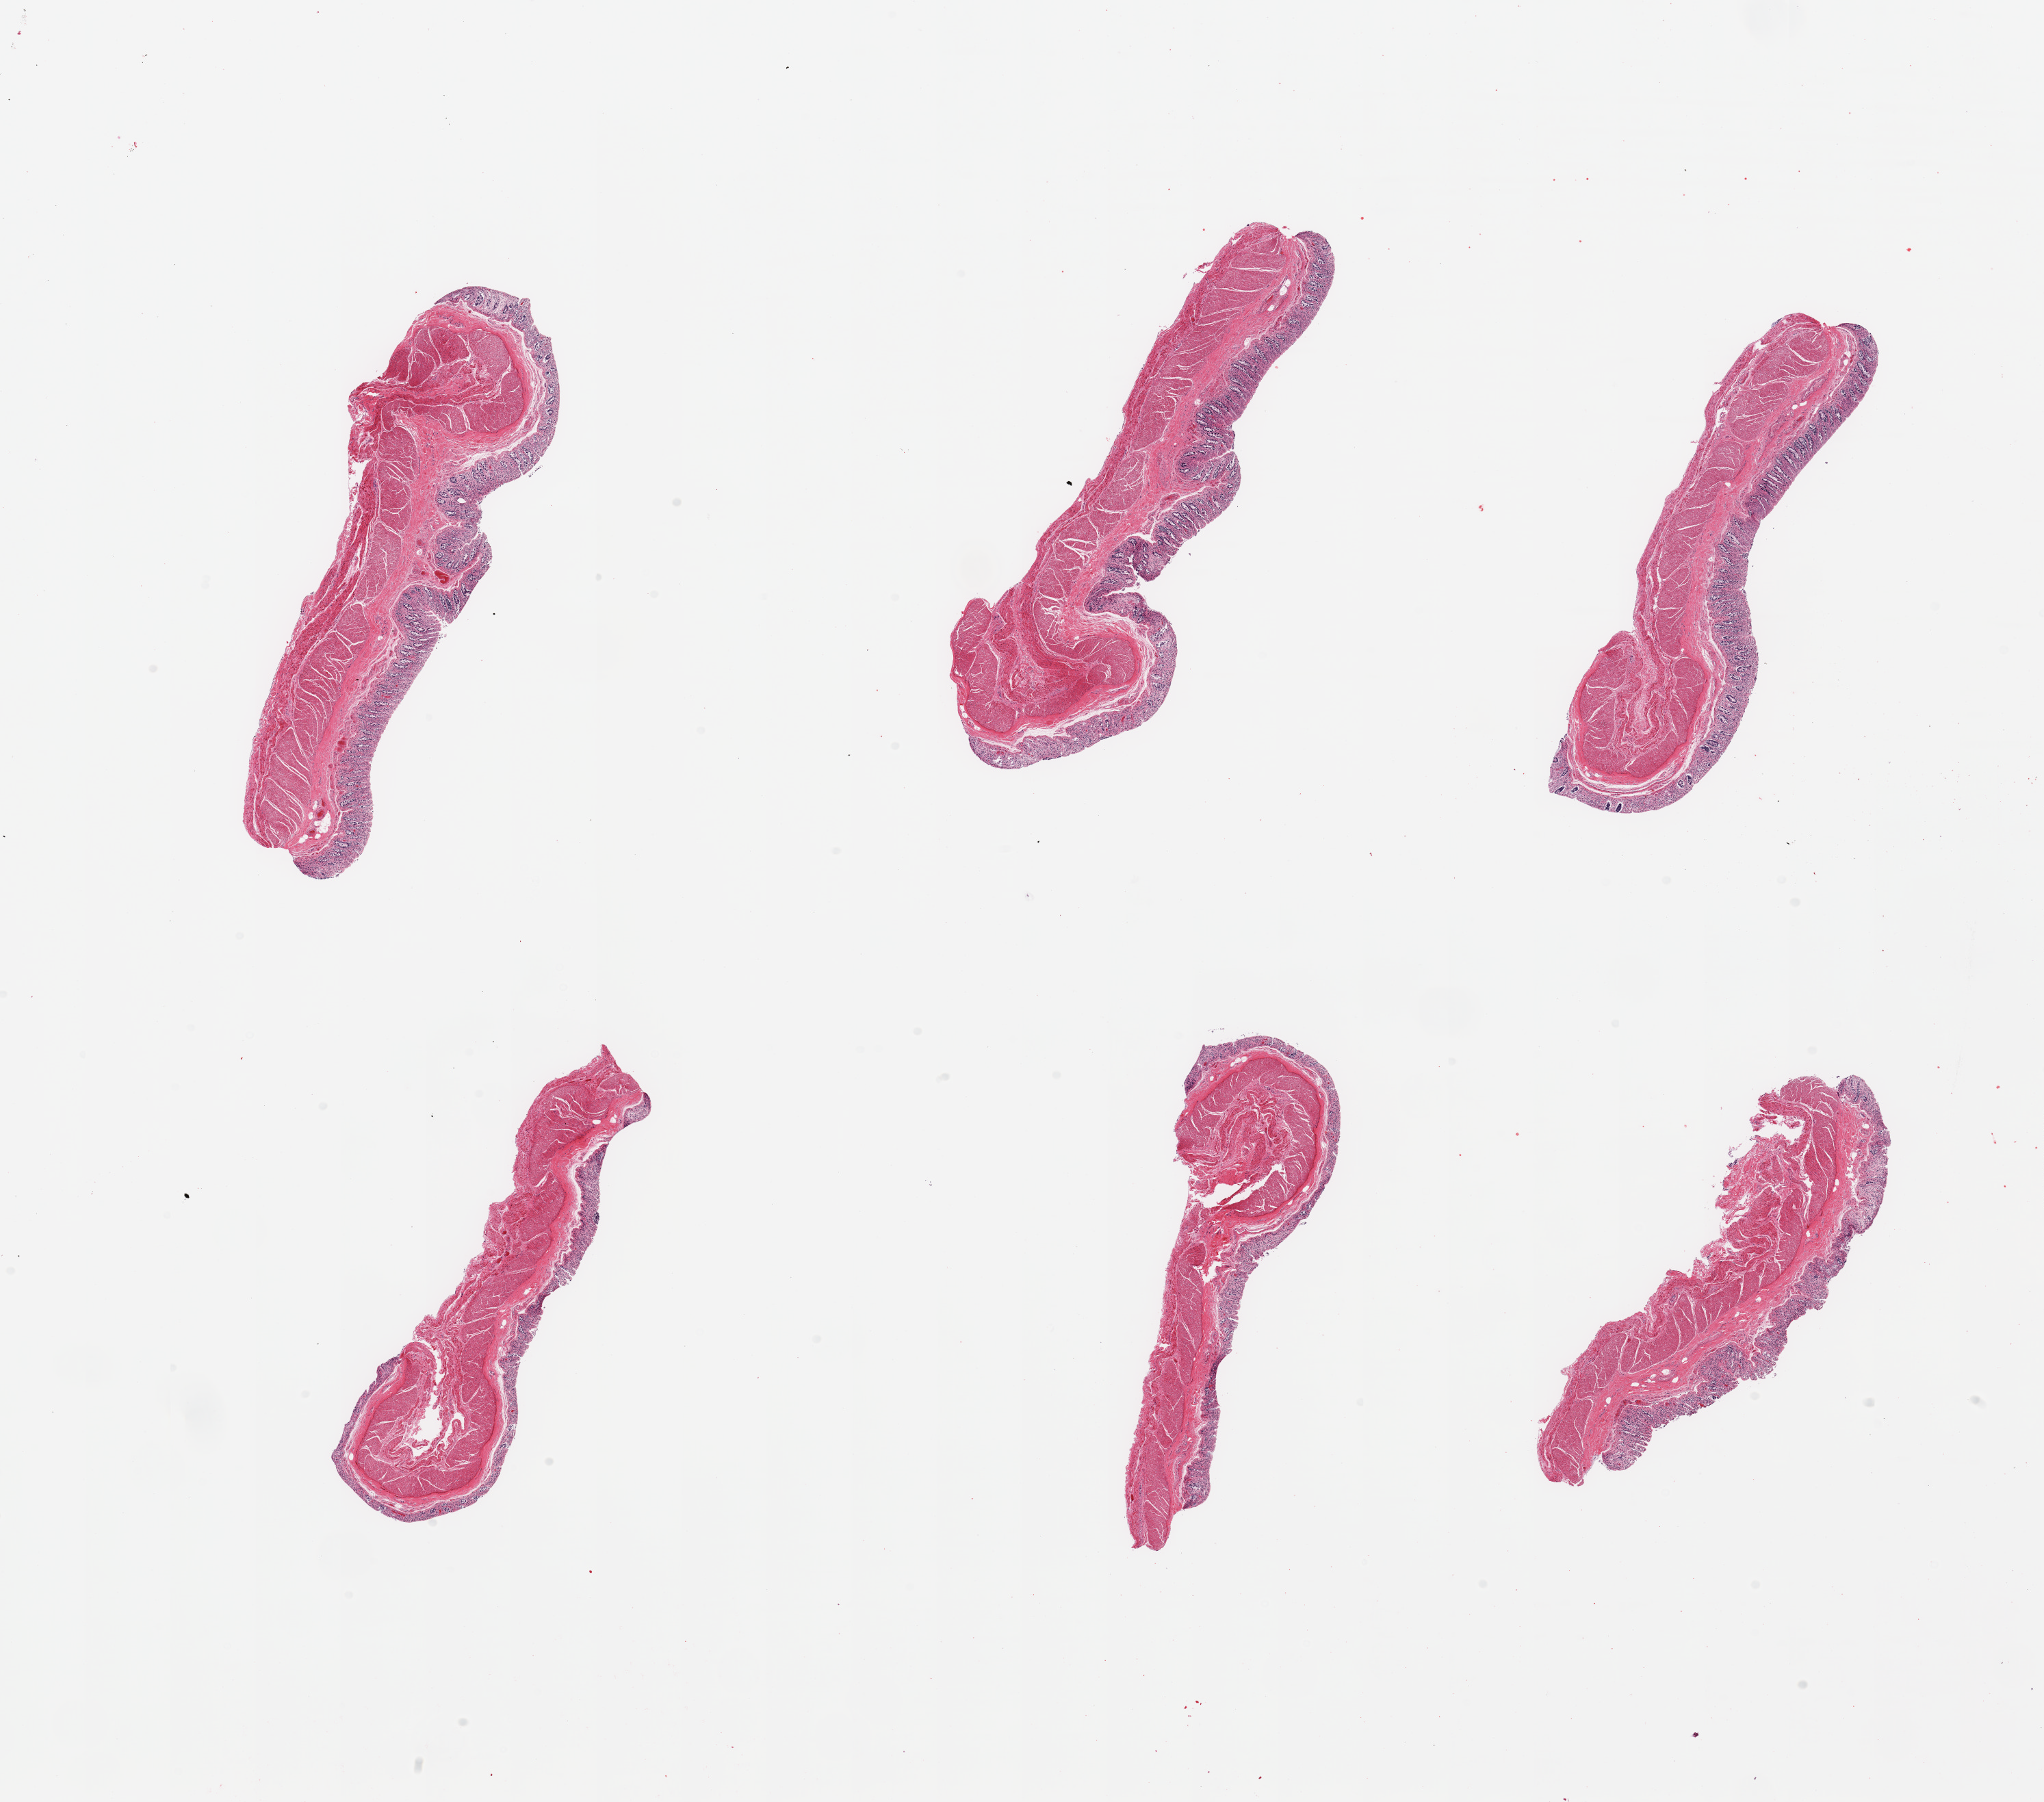
Hematoxylin and eosin (H&E) whole-slide image, low-resolution overview of the scanned area, about 23.6 x 20.8 mm (from a 20x scan); PAXgene-fixed, paraffin-embedded tissue; target tissue: transverse colon; tissue donor sample.
Reviewer comment on this tissue sample: 6 pieces; mucosa largely autolyzed; muscularis intact.